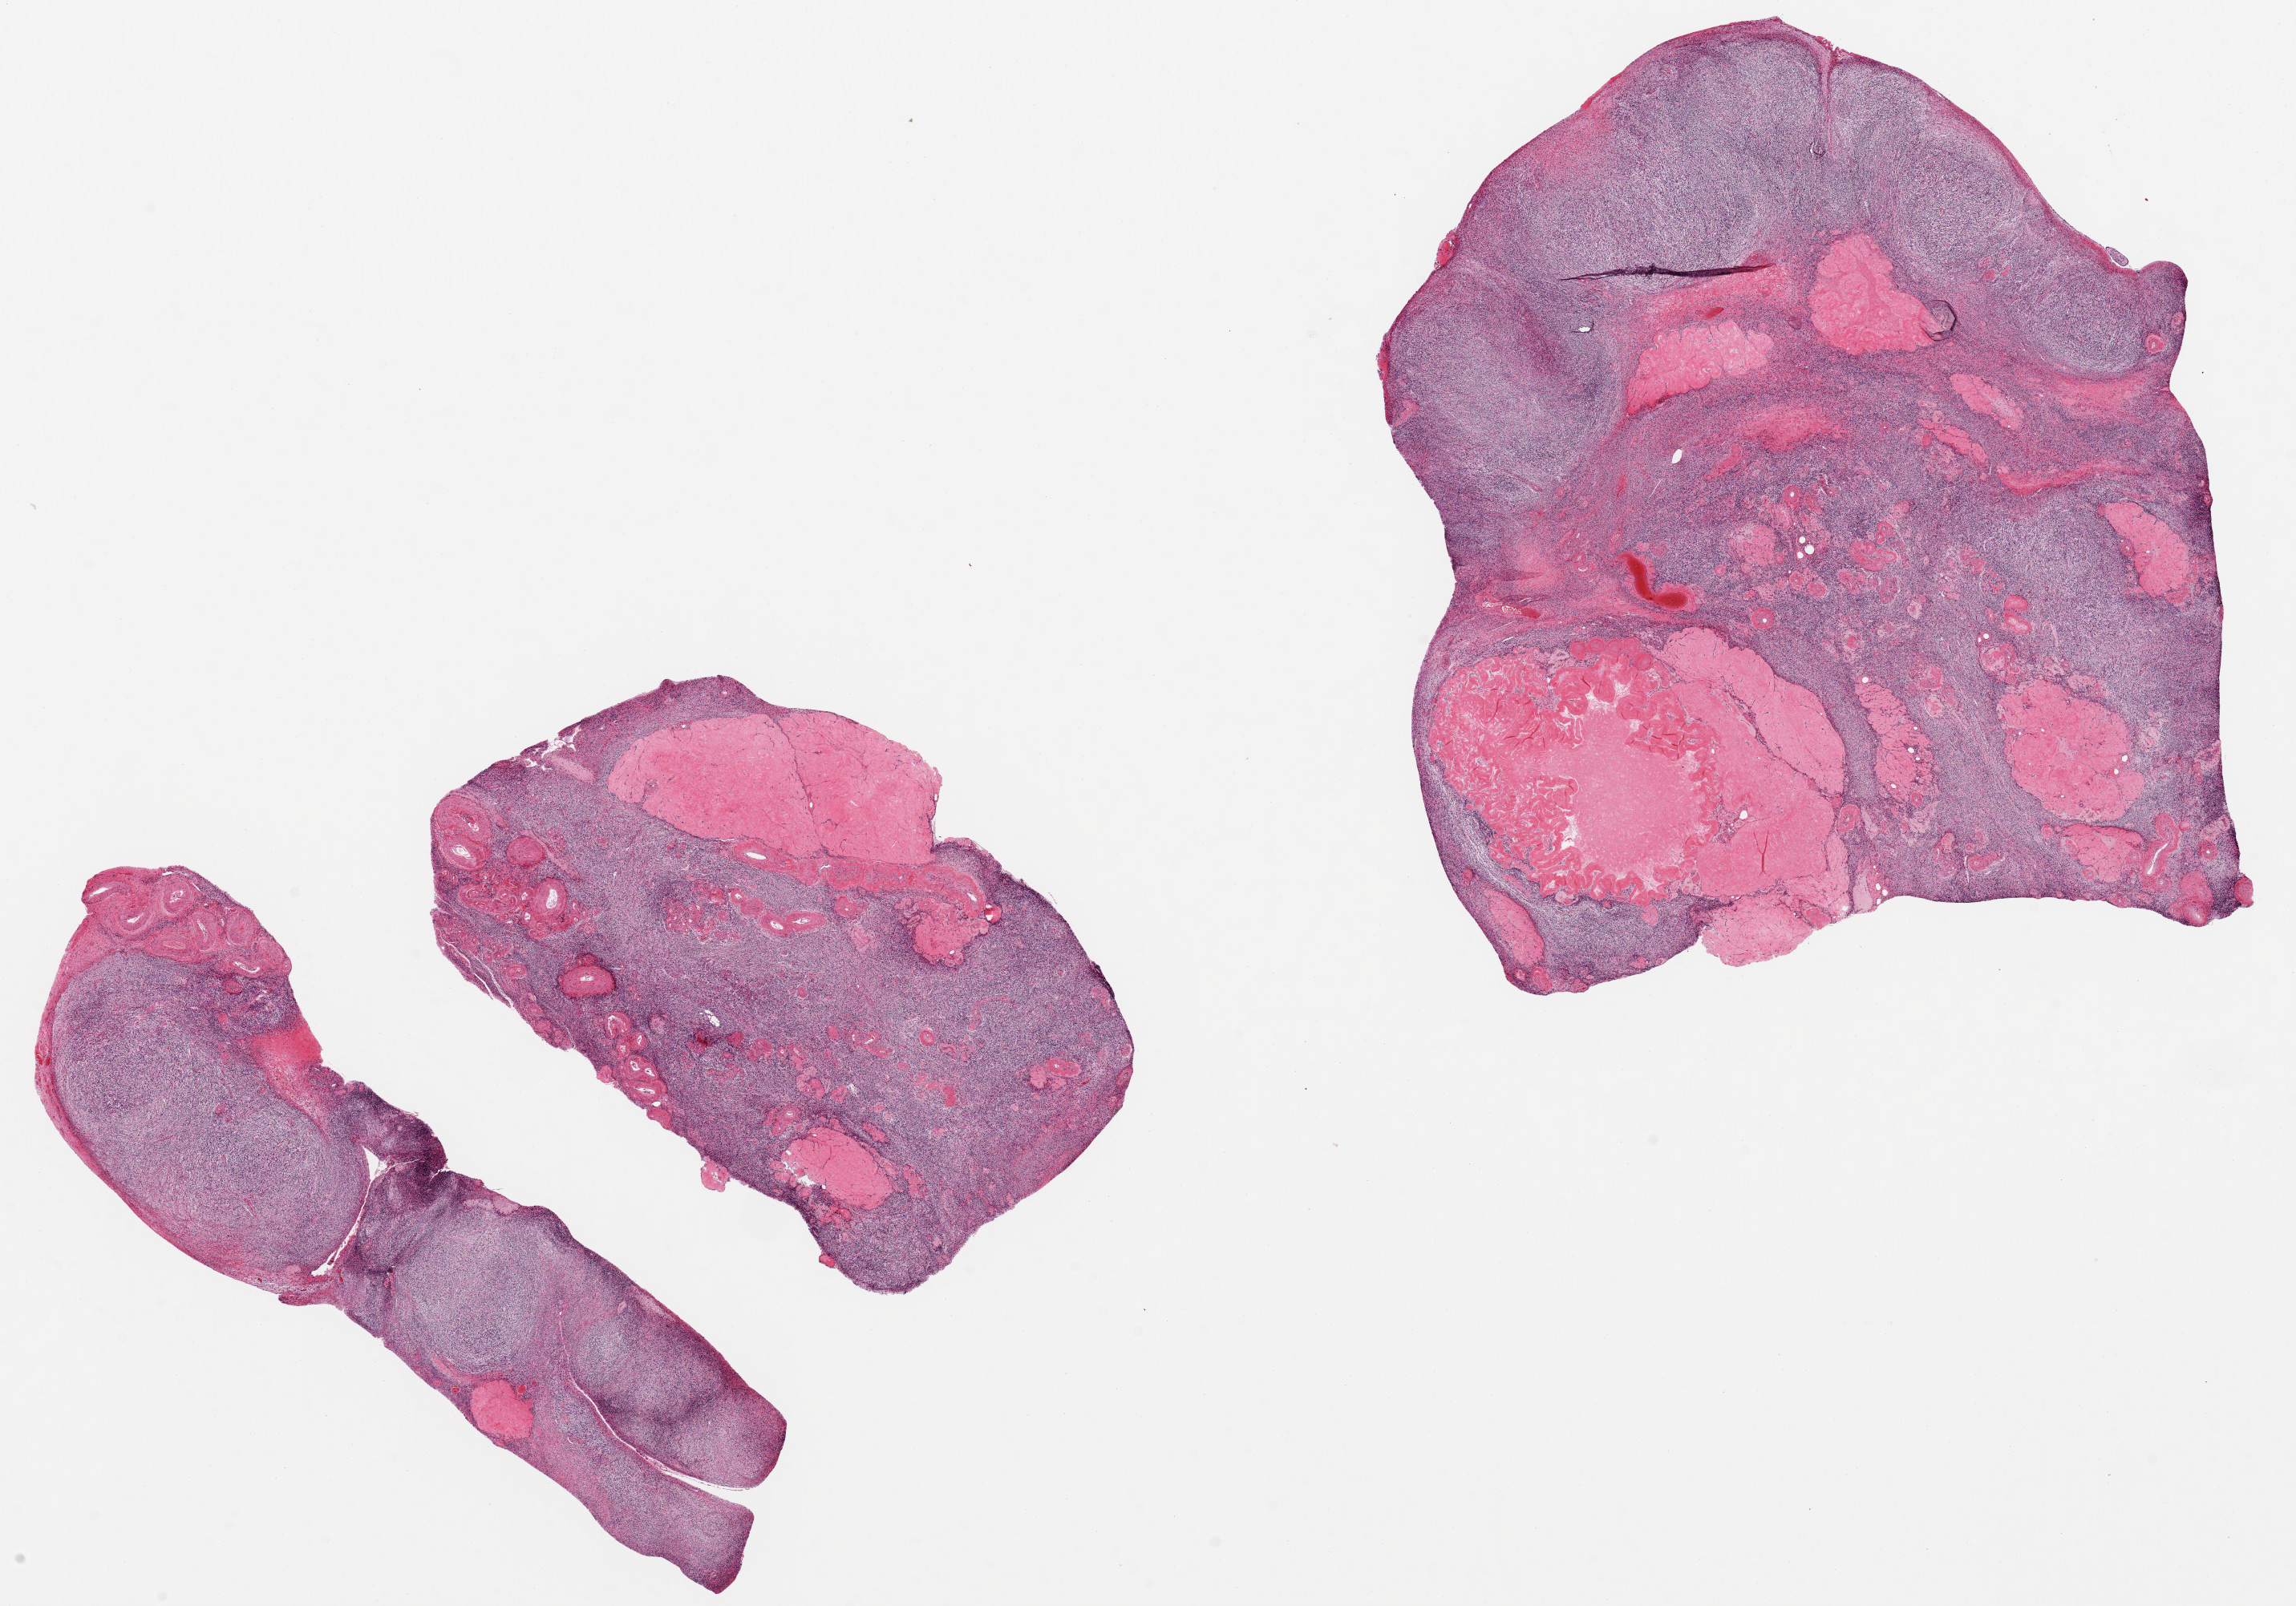
Digitized H&E-stained section, shown as a low-resolution overview of the whole scanned area (about 22.6 x 15.8 mm, acquisition: 20x scan); PAXgene-fixed, paraffin-embedded tissue; section of ovary (target tissue); donor tissue sample. Female donor.
Pathologist's review note for this sample: 2 pieces. 9x8 & 9x8mm; atrophic, several corpora albicans.